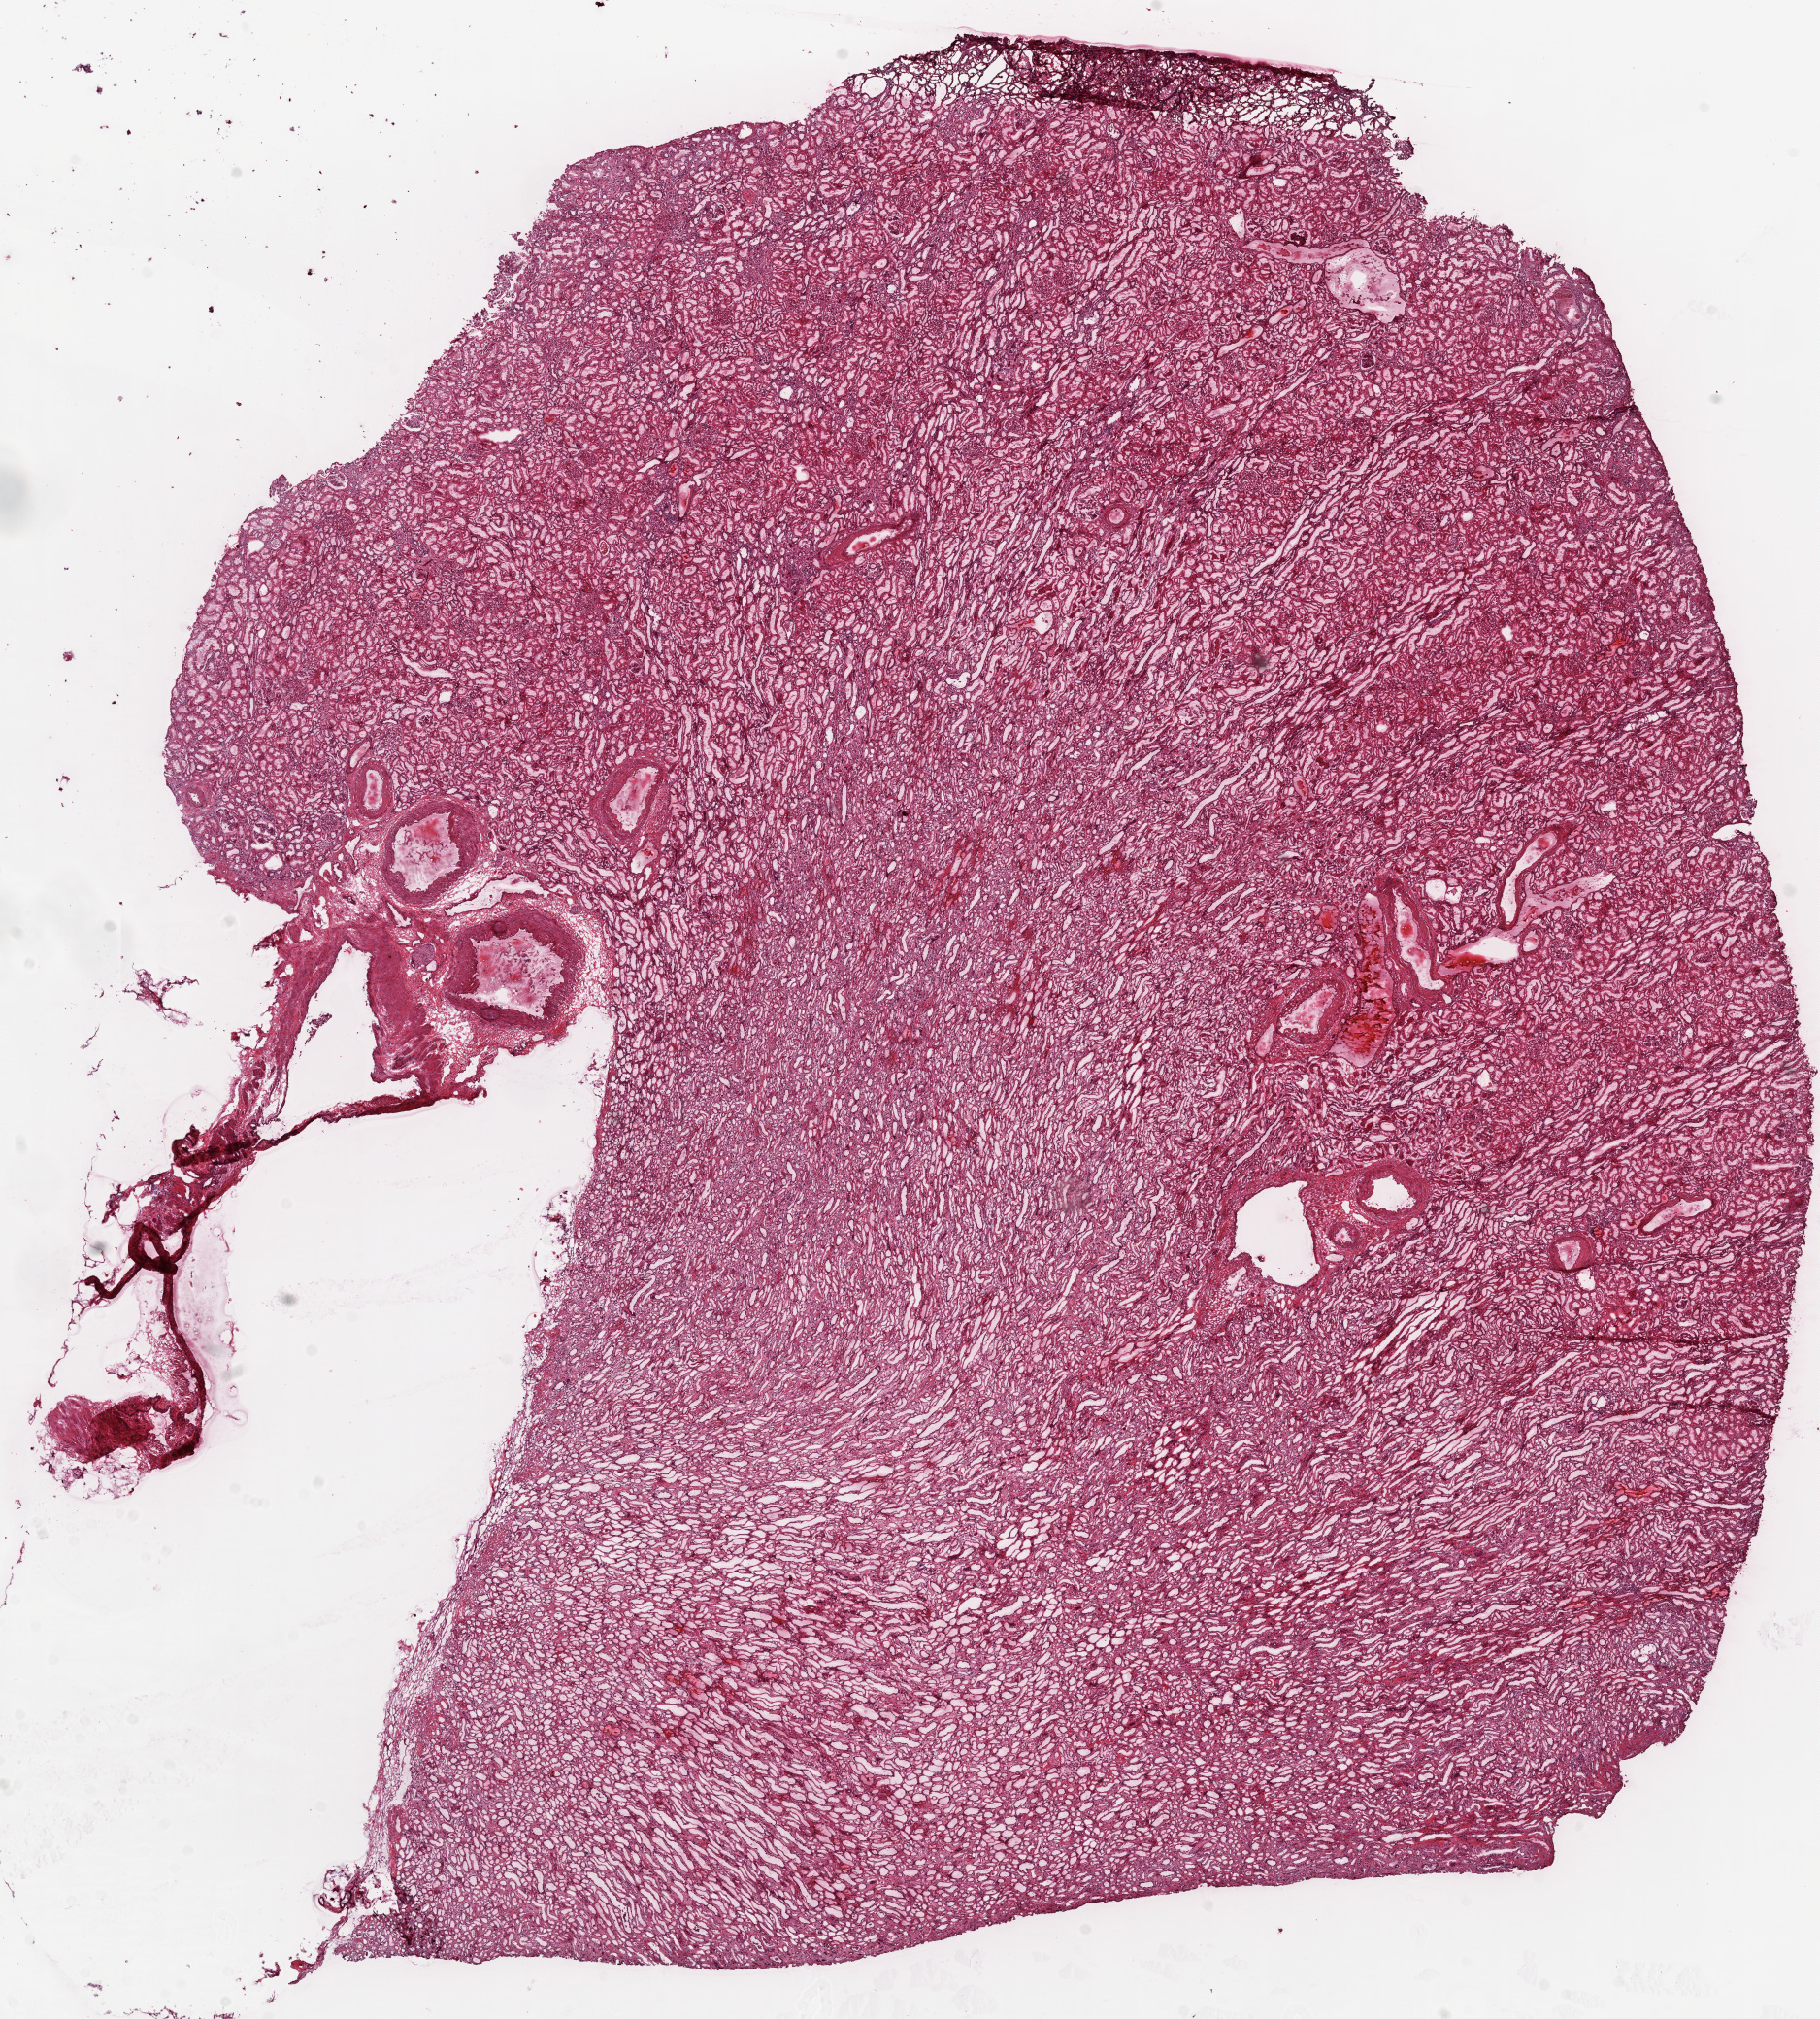
H&E whole-slide image — low-resolution overview of the scanned area, about 15.0 x 16.7 mm (from a 20x scan); frozen section; solid tissue normal (non-tumour tissue) sample from the kidney. Female patient; age at initial diagnosis 59 years.
* this section: solid tissue normal sample (biorepository sample class)
* patient diagnosis: Clear cell adenocarcinoma, NOS